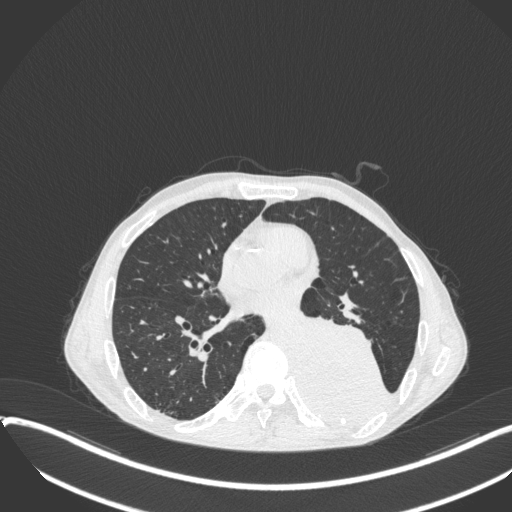
Chest CT, one axial slice; slice 165 of 400 in the series (ordered by position); reconstruction kernel B31f; 120 kVp; lung window (W 1500 / L -600 HU); 512 × 512 image matrix, field of view 400 × 400 mm. Patient: male, 57 years. From the clinical record (not read from this slice): clinical TNM (as recorded): T4 N0 M0.
Annotated regions visible in this slice (rectangle marked by the reading radiologist):
- lung tumour (recorded histology: squamous cell carcinoma): bounding box <294,306,394,429> (left, top, right, bottom; pixels)